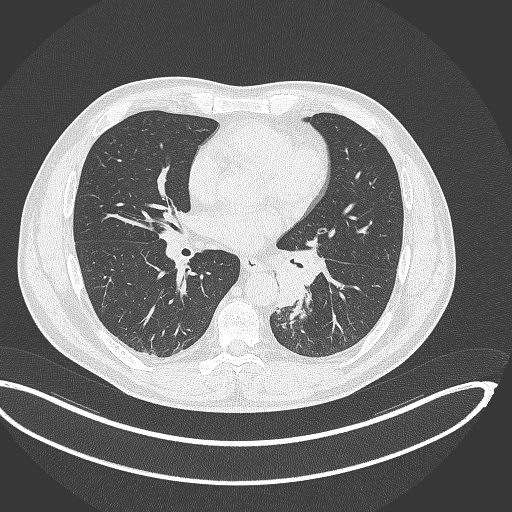
Chest CT, one axial slice; position 171 of 362 along the scan axis; lung window (W 1500 / L -600 HU); 1 mm slice thickness; 512 × 512 image matrix, field of view 442 × 442 mm. Patient: male, 50 years. From the clinical record (not read from this slice): clinical TNM (as recorded): T2a N3 M0.
Structures marked on this image (bounding box drawn by a radiologist):
- lung tumour (recorded histology: squamous cell carcinoma): bounding box (x1, y1, x2, y2) in pixels: (269, 242, 326, 308)